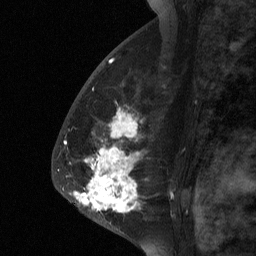
Breast MRI (dynamic contrast-enhanced), one sagittal slice. Slice 40 of 64 in the series (ordered by position). Dynamic contrast-enhanced study with each time point stored as its own series, time point 2 of 3 at this slice position (early post-contrast, ordered by acquisition time). 1.5 T. TE 4.8 ms, TR 27 ms. 2 mm slice thickness. 256 × 256 image matrix. Patient: female, 56 years. Case-level facts recorded for this patient, not image findings: setting: breast cancer imaged before/during neoadjuvant chemotherapy; receptor status: HER2-positive.
Annotated regions visible in this slice (semi-automatically segmented with operator editing):
- analysis volume of interest (the breast-tissue region the enhancement analysis was run in; not a lesion): bounding box <68,104,182,229> (left, top, right, bottom; pixels)
- tumour enhancement mask (voxels above the 90 % enhancement threshold inside the analysis volume of interest): <73,116,139,212>